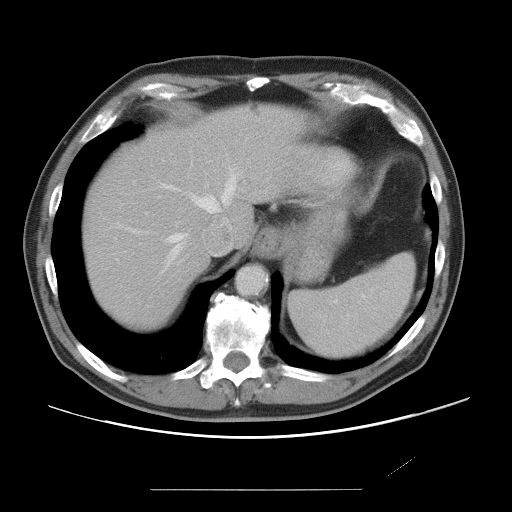
Contrast-enhanced abdominal CT, one axial slice; slice 61 of 87 in the series (ordered by position); 120 kVp; intravenous contrast given; soft-tissue window (W 400 / L 40 HU); 5 mm slice thickness; 512 × 512 image matrix. Male patient, age 74 years. Case-level facts recorded for this patient, not image findings: diagnosis: colorectal cancer liver metastases, imaged before liver resection; multiple liver metastases: yes; largest metastasis: 1.1 cm; disease in both lobes: no.
Outlined on this slice (expert manual segmentation):
- hepatic veins: bounding box (x1, y1, x2, y2) in pixels: (126, 175, 236, 256)
- liver: (83, 106, 316, 328)
- planned liver remnant (the part of the liver to remain after resection): (83, 107, 318, 328)
- liver metastasis: (250, 105, 260, 113)